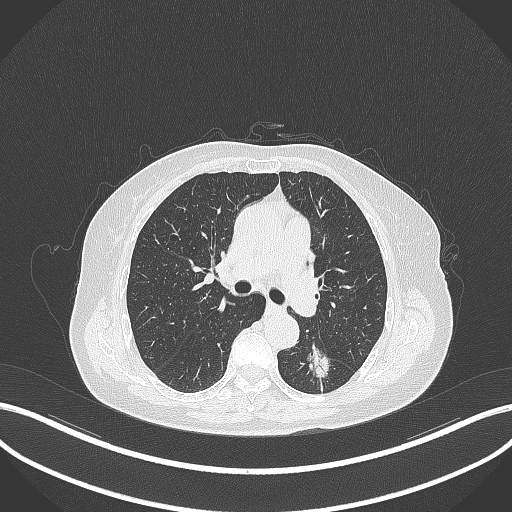
Chest CT, one axial slice; position 181 of 352 along the scan axis; 120 kVp; lung window (W 1500 / L -600 HU); 1 mm slice thickness; 512 × 512 image matrix, field of view 400 × 400 mm. Patient: female, 70 years. Case-level facts recorded for this patient, not image findings: clinical TNM (as recorded): T1c N0 M0.
Structures marked on this image (rectangle marked by the reading radiologist):
- lung tumour (recorded histology: adenocarcinoma): box from (x=305, y=340) to (x=335, y=384) px